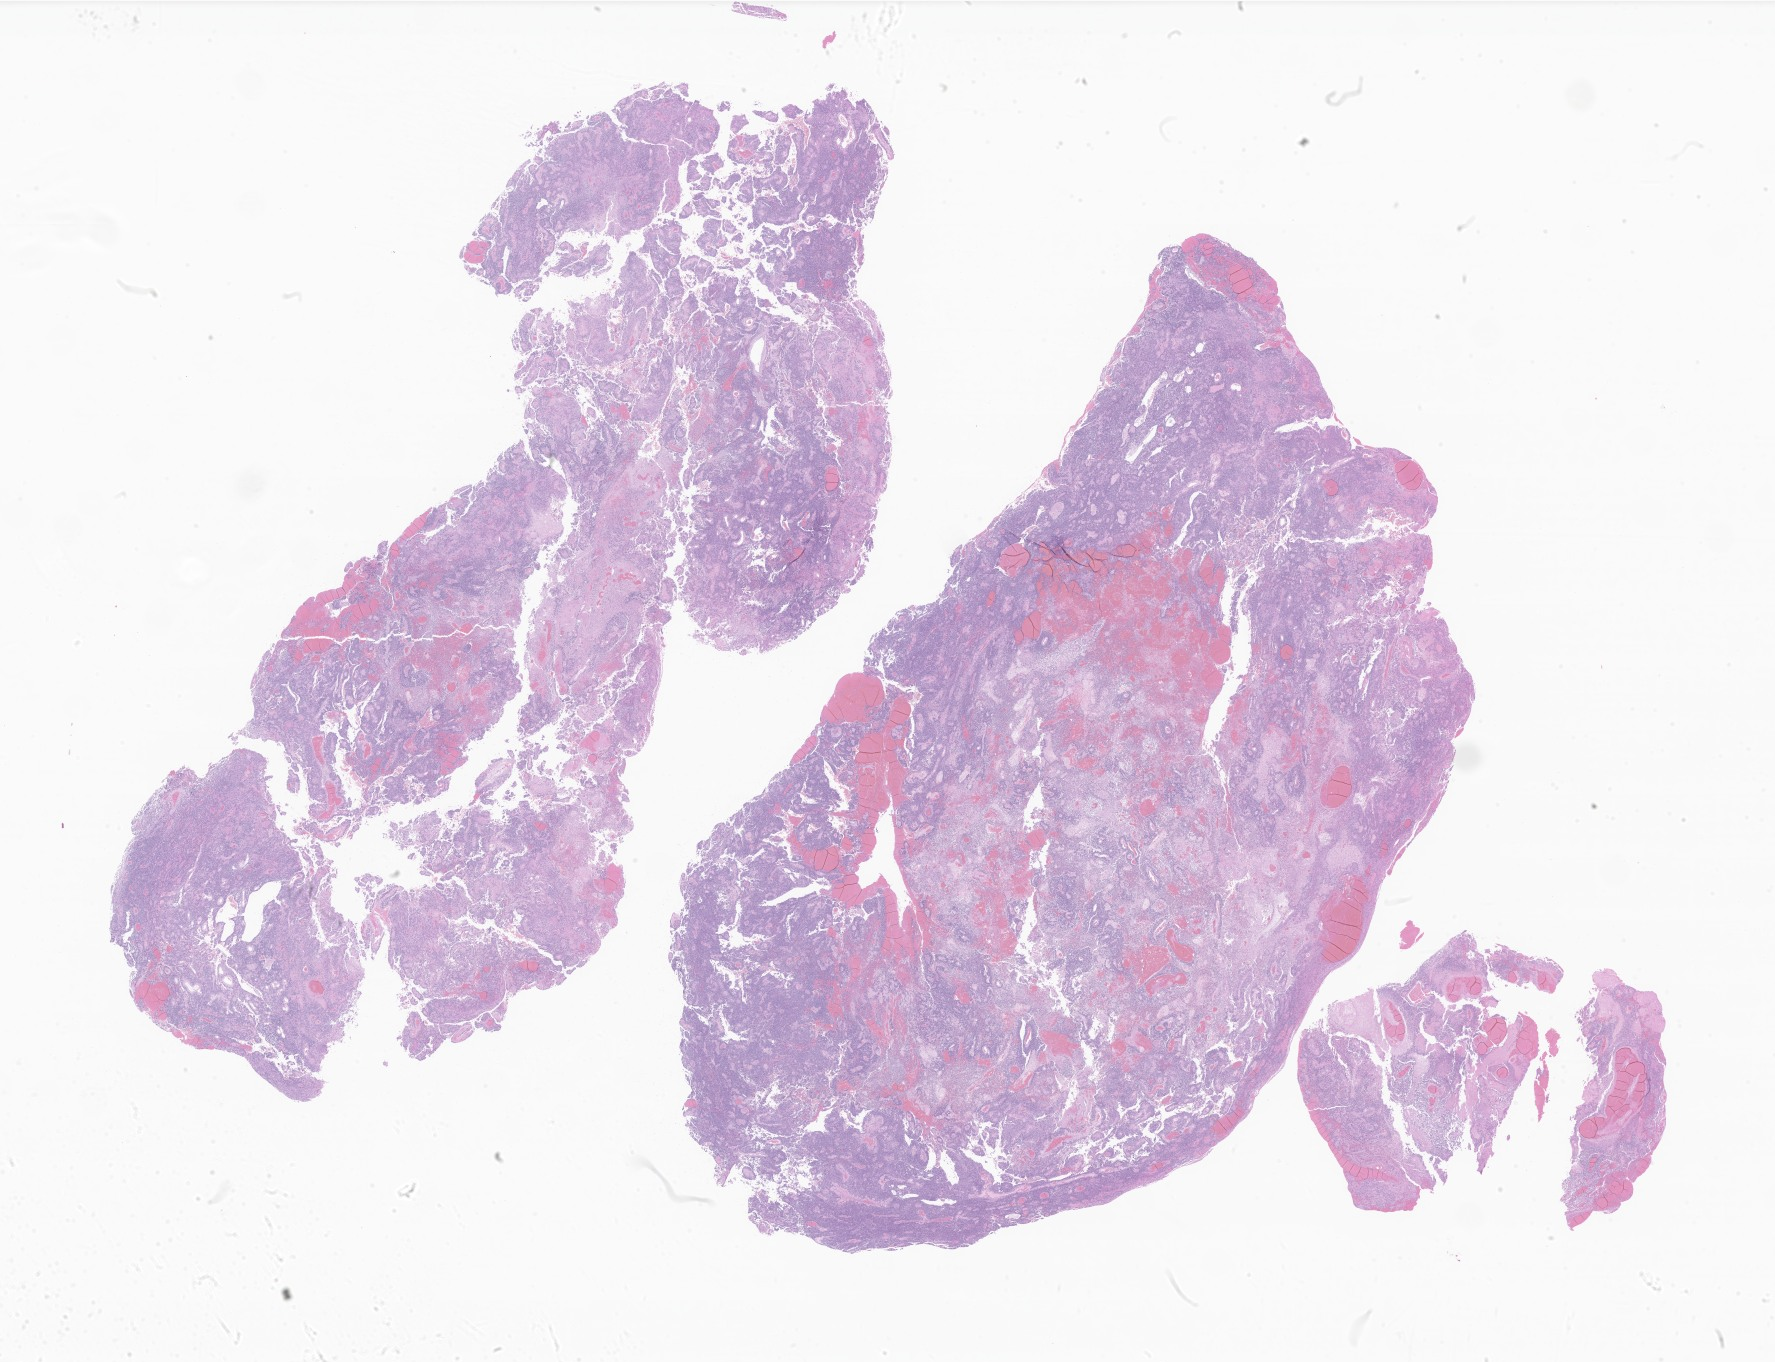
Whole-slide image, H&E stain of tumor tissue from the brain, a low-resolution overview of the entire scanned area, about 29.9 x 23.0 mm, formalin-fixed, paraffin-embedded (FFPE) tissue. Female patient, age 181 months (15 years 1 month).
- diagnosis: Ependymoma, NOS